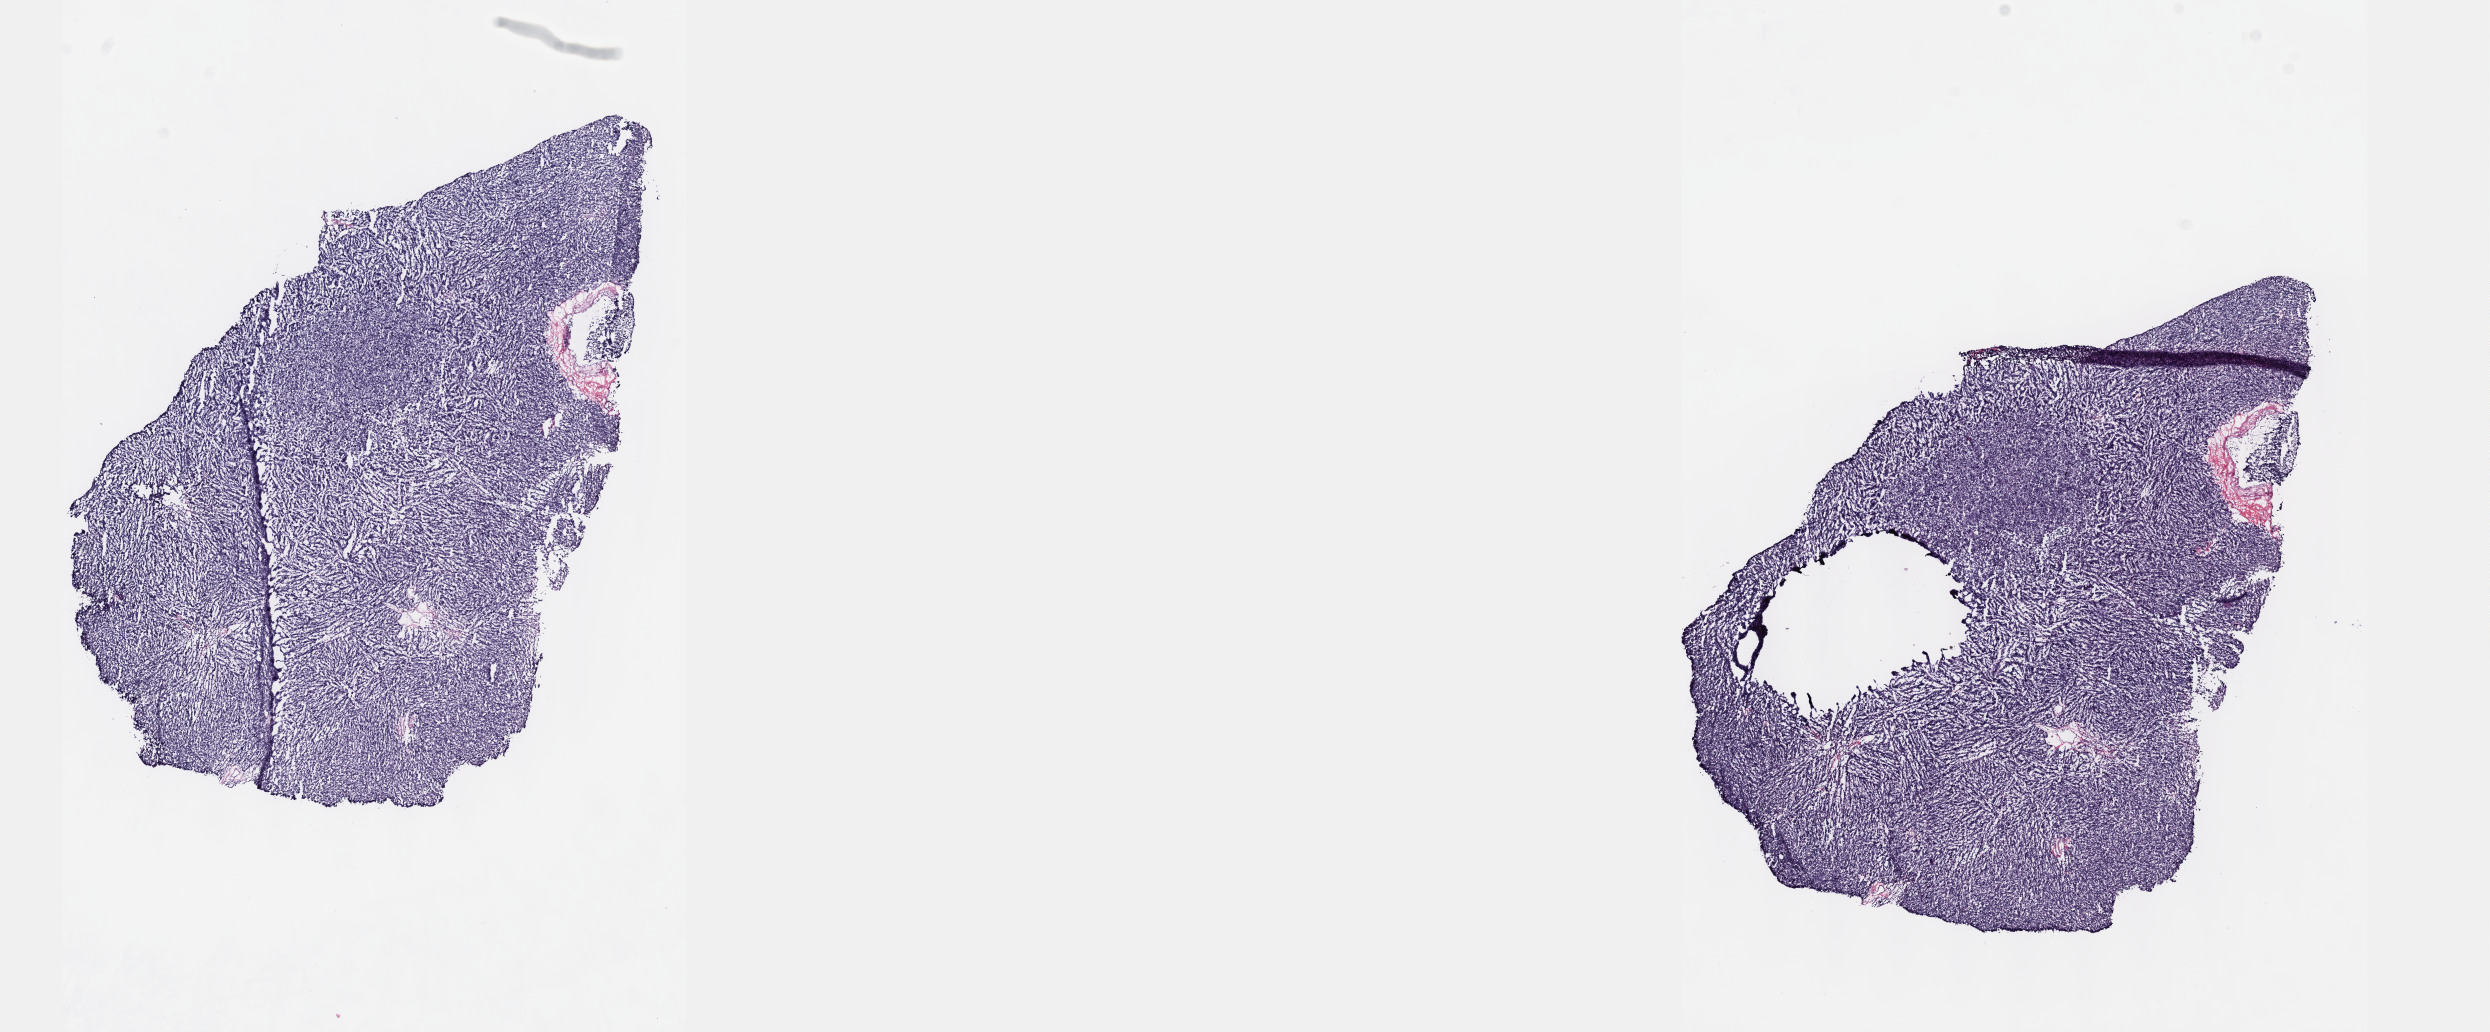
Digitized Hematoxylin and eosin (H&E) stained tissue section (whole slide), whole scanned area (about 20.1 x 8.3 mm) shown as a low-resolution overview, frozen section from the top of the tissue portion, thymus, primary tumour sample. Female patient; age at initial diagnosis 54 years. Composition of this section per pathologist review: tumour cells 99%, tumour nuclei 99%, normal cells 0%, stromal cells 1%, necrosis 0%. Inflammatory infiltration, as recorded: lymphocyte infiltration 0%, monocyte infiltration 0%, neutrophil infiltration 0%.
Diagnosis: Thymoma, type B1, malignant.